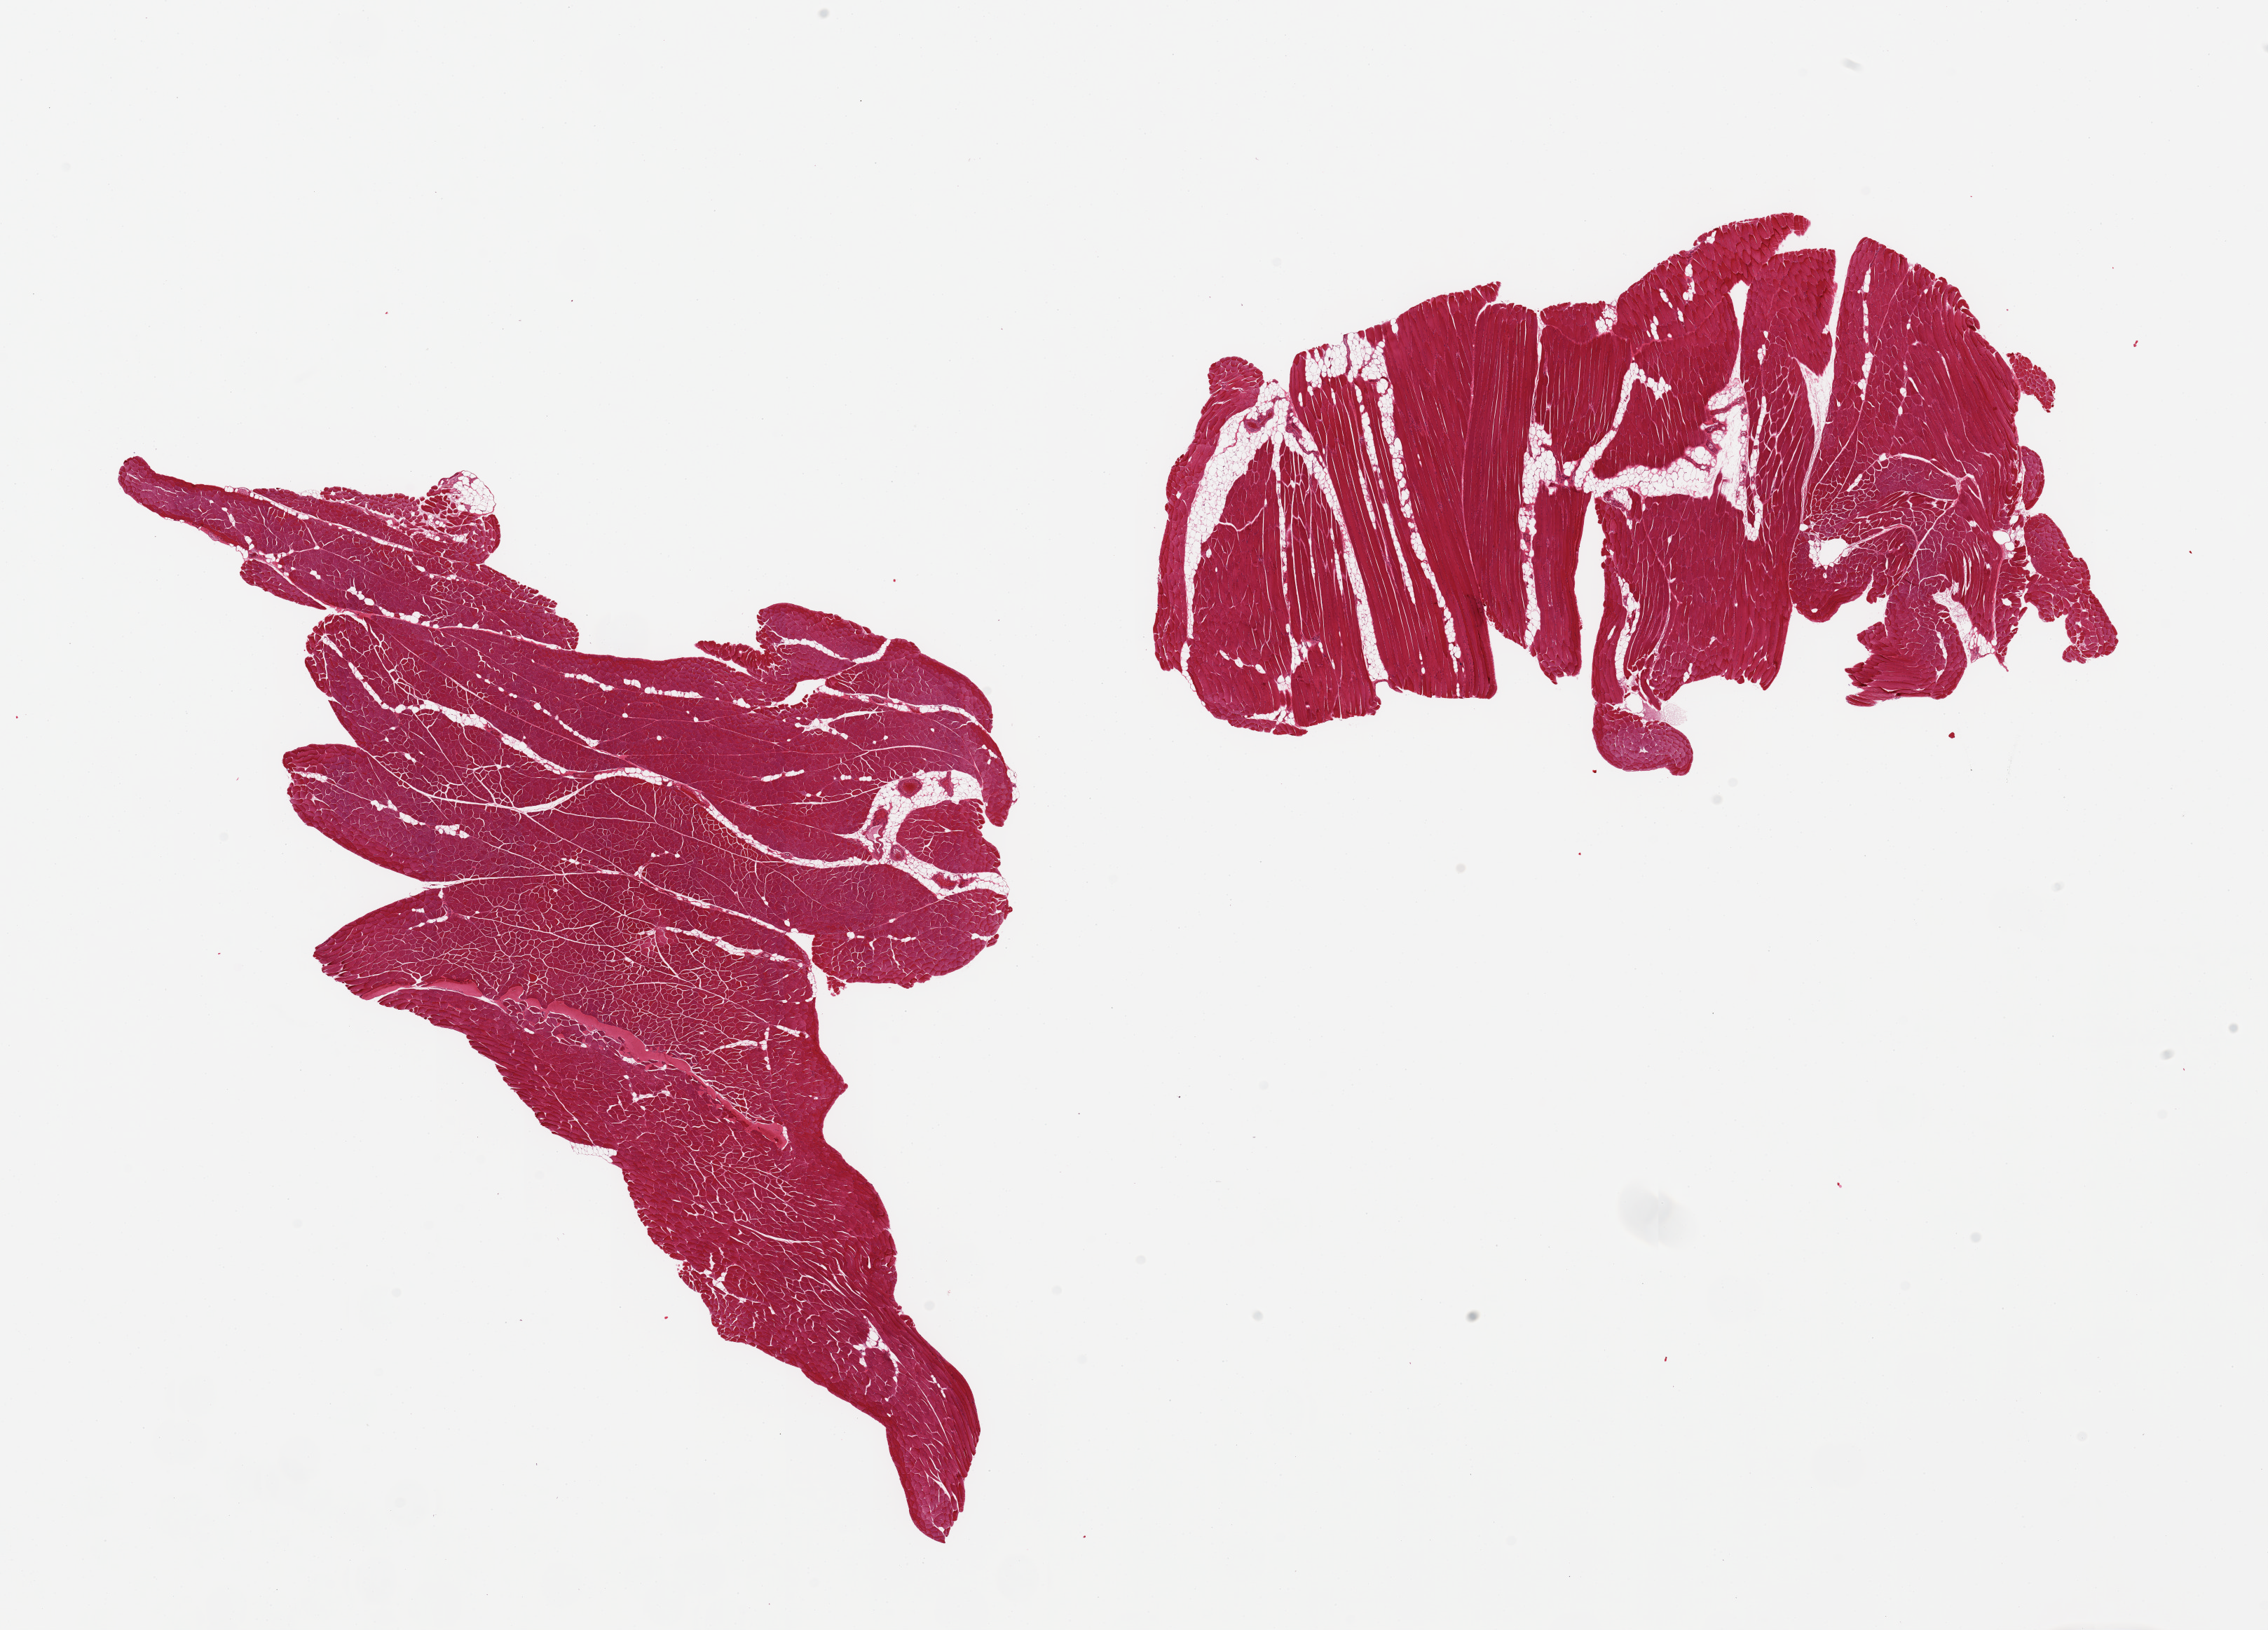
Digitized H&E-stained section, a low-resolution overview of the entire scanned area, about 25.6 x 18.4 mm. PAXgene-fixed paraffin-embedded (PFPE) section. Sampled site (target tissue): skeletal muscle. Tissue donor sample. Donor sex: male.
Reviewer comment on this tissue sample: 2 pieces; up to 10 to 20% internal fat, small portion of tendon.